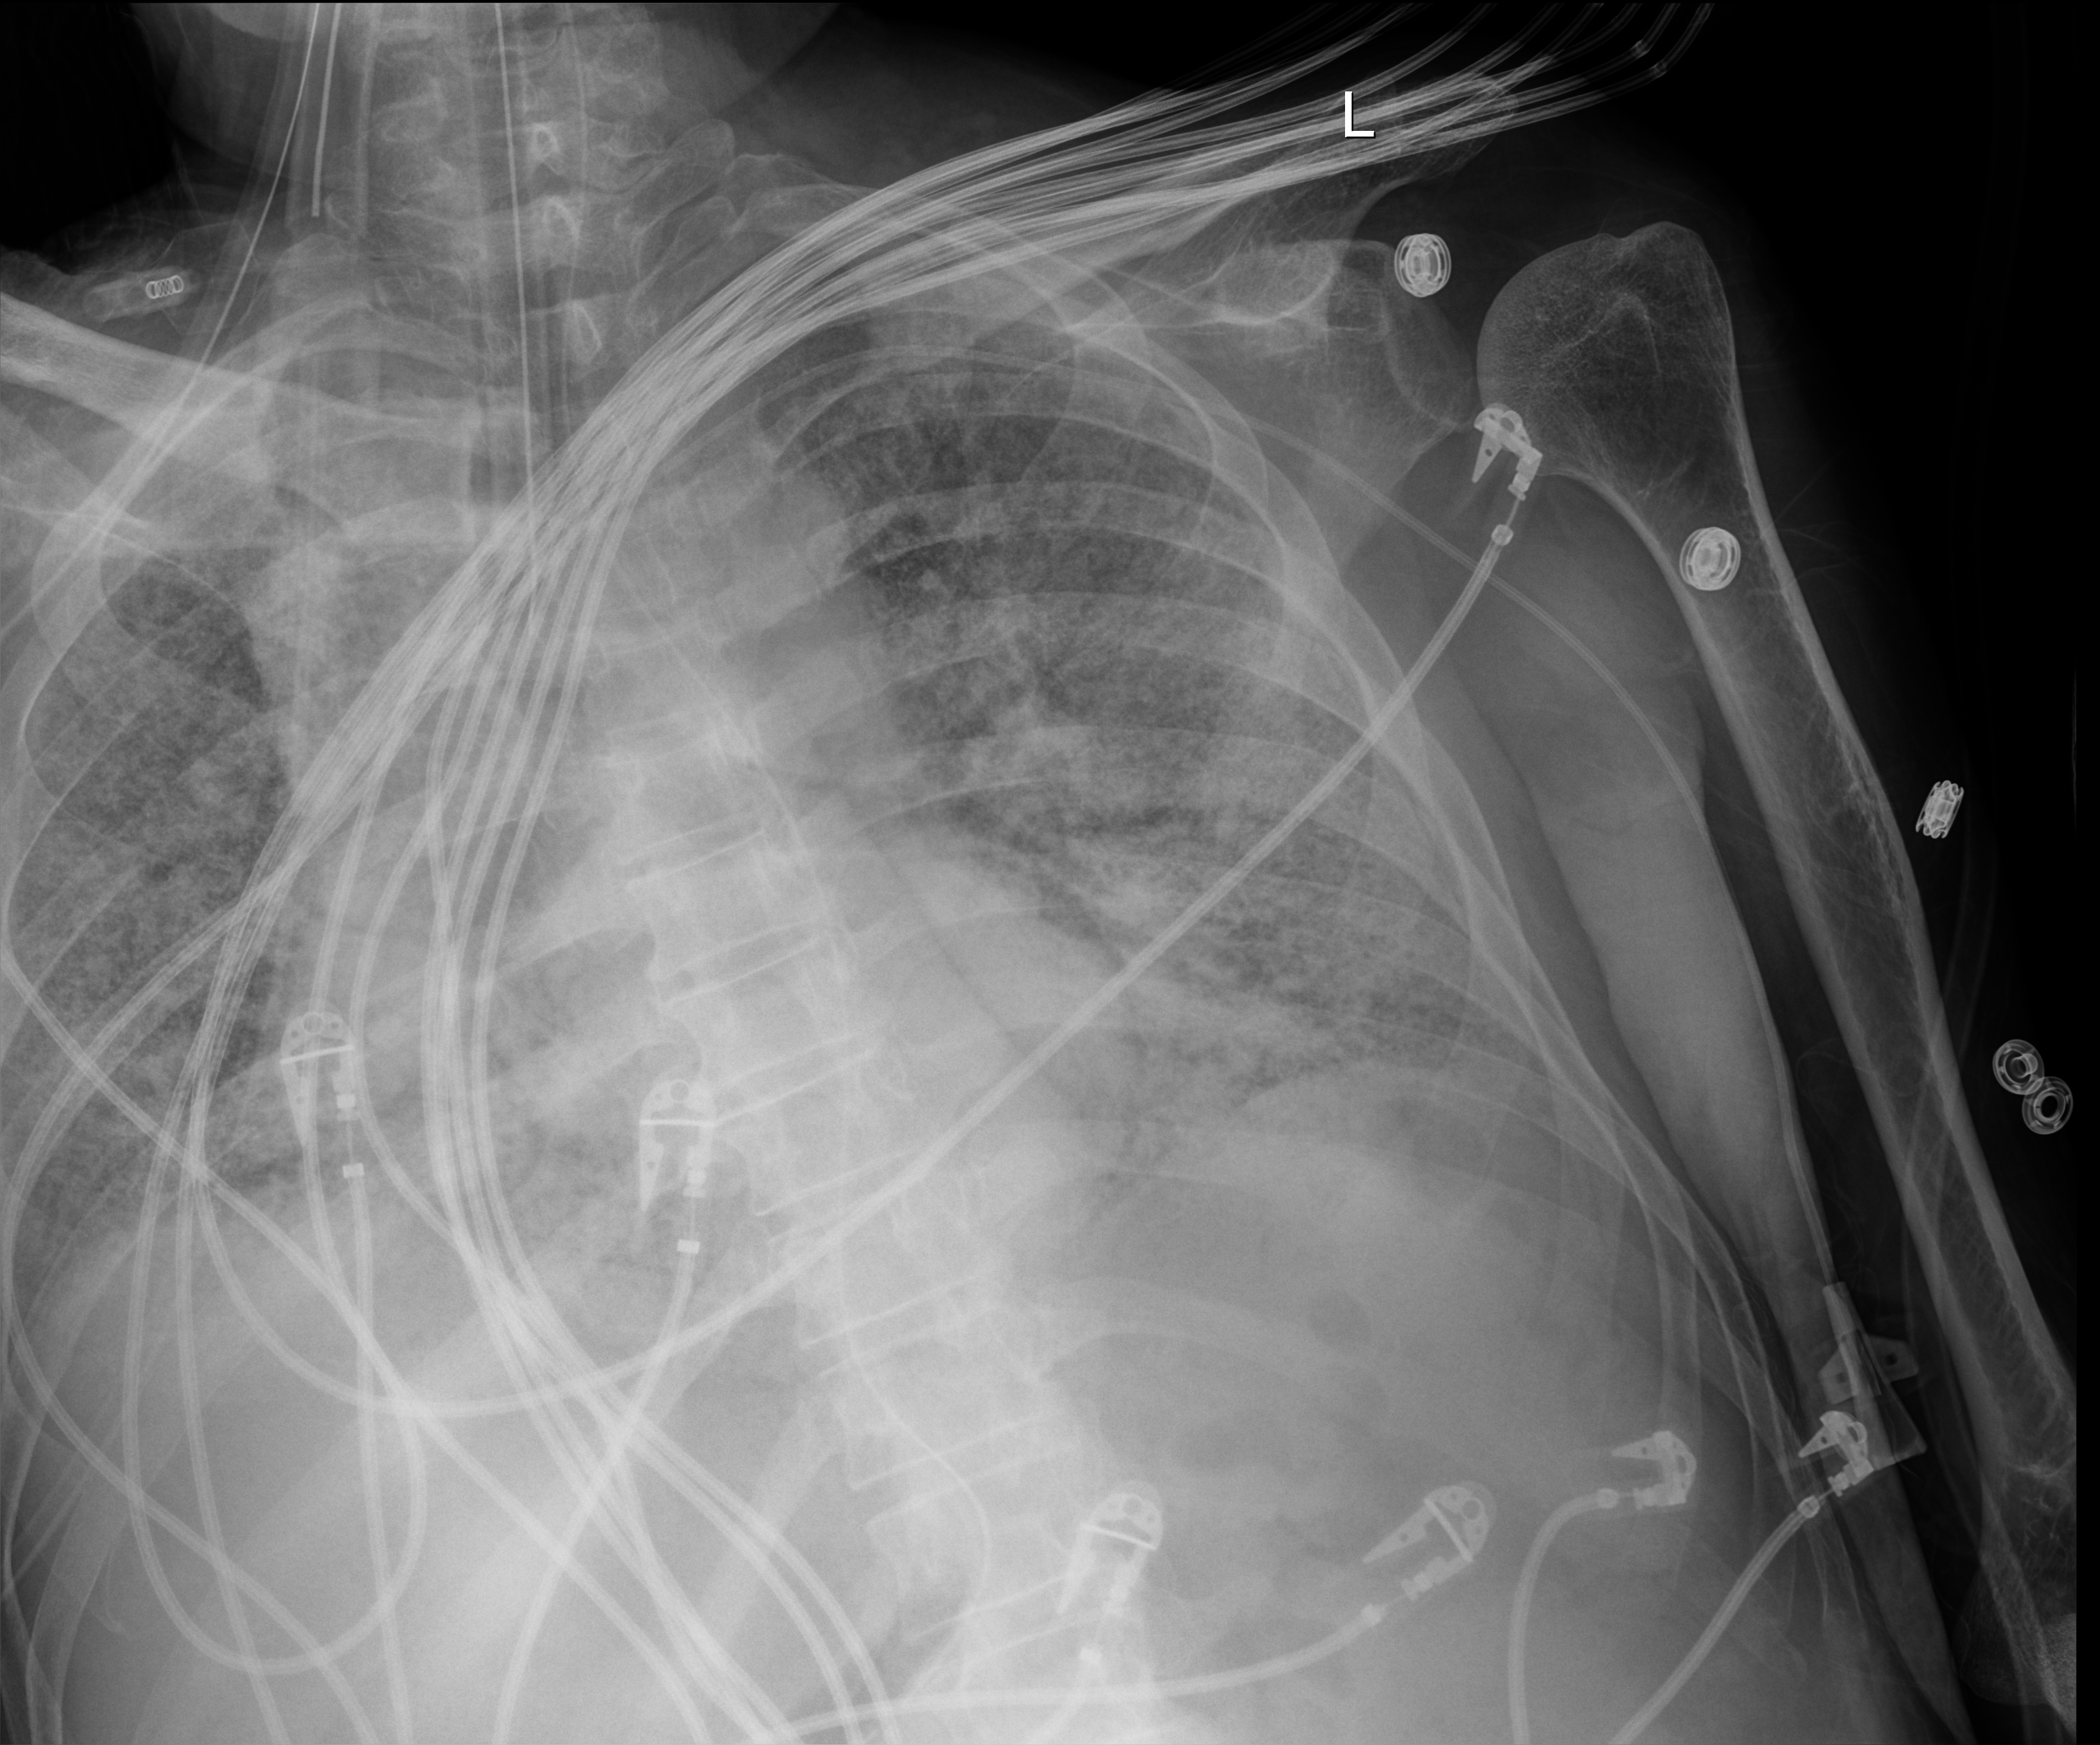
Chest X-ray; anteroposterior (AP) projection. Patient hospitalised with COVID-19; male, aged 60–74 years.
Admission-level facts for this patient (not findings on this image; timing relative to this image not recorded): length of hospital stay: 54 days; admitted to intensive care during this hospital stay: yes.